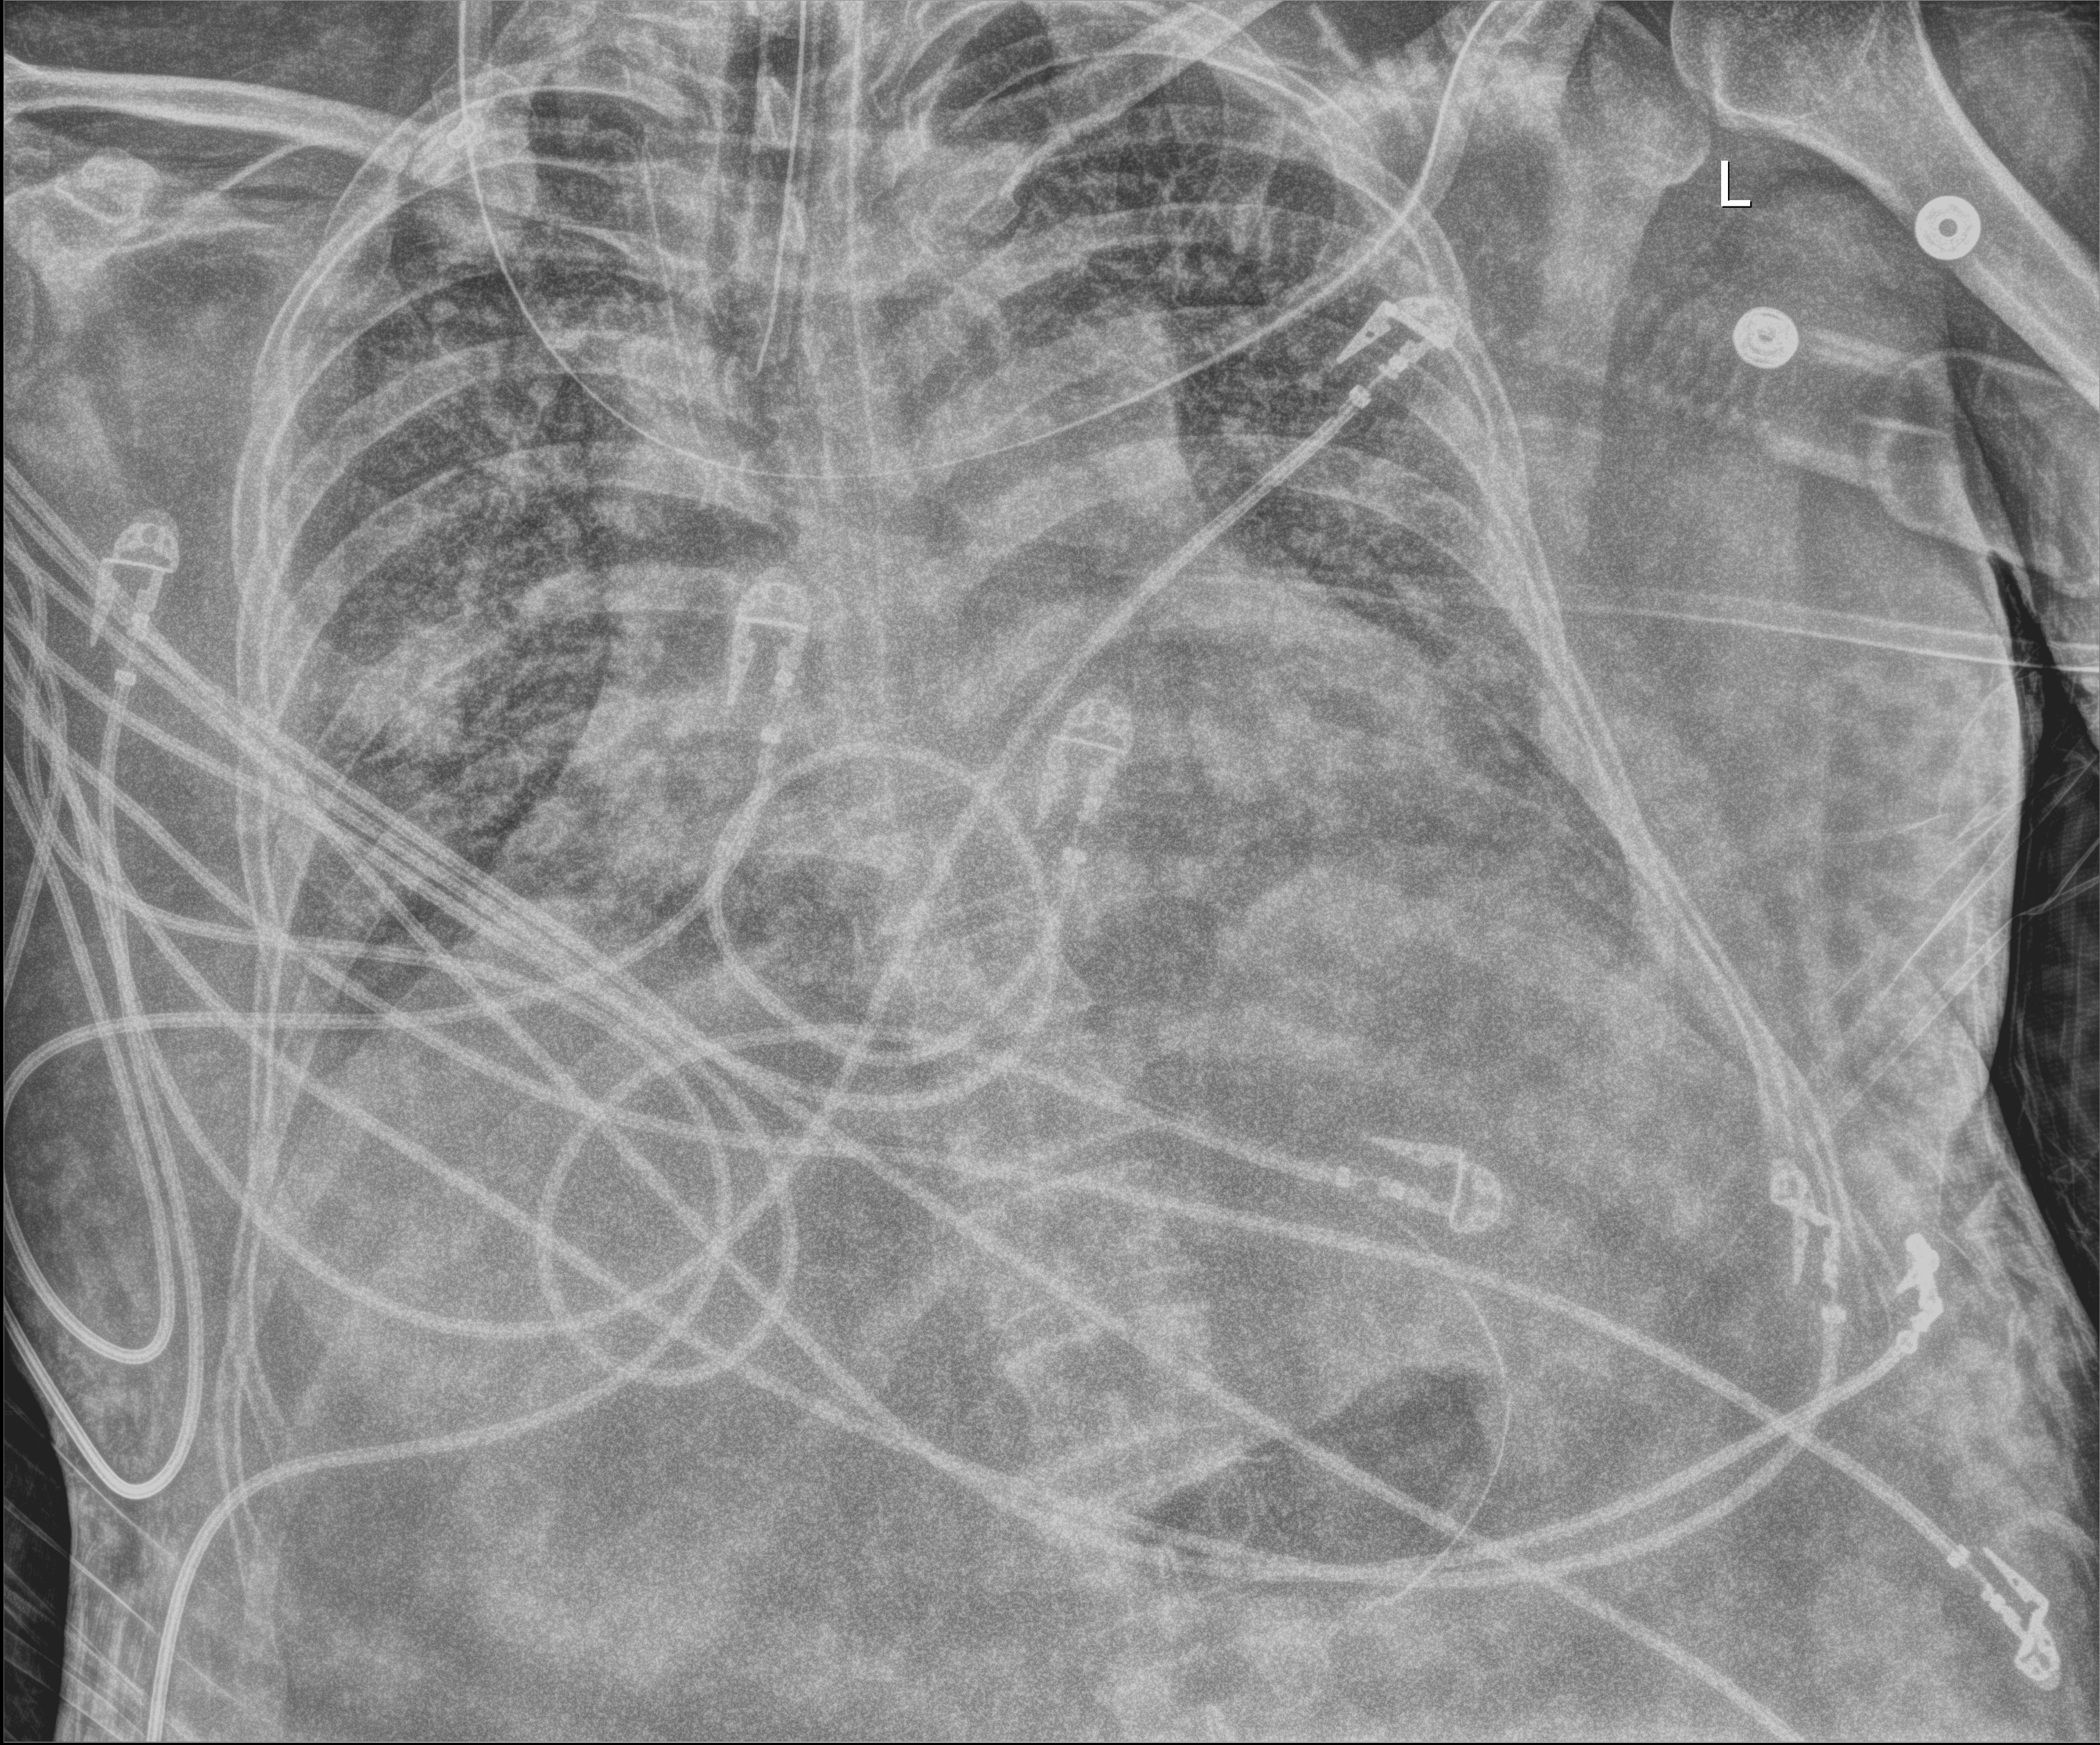
Chest X-ray (portable); anteroposterior (AP) projection. Patient hospitalised with COVID-19, aged 18–59 years.
From the hospital-stay record, not from the radiograph (when in the stay this image was taken is not recorded):
- admitted to intensive care during this hospital stay: yes
- mechanically ventilated during this hospital stay: yes